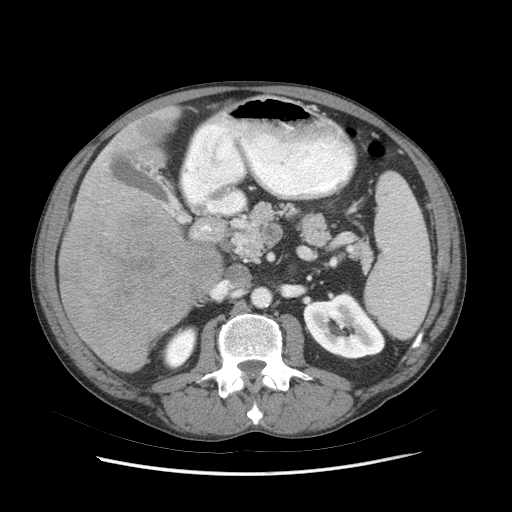
Contrast-enhanced abdominal CT (liver protocol), one axial slice; slice 31 of 89 in the series (ordered by position); reconstruction kernel STANDARD; 140 kVp; soft-tissue window (W 400 / L 40 HU); 2.5 mm slice thickness; 512 × 512 image matrix, field of view 380 × 380 mm. Case-level facts recorded for this patient, not image findings: diagnosis: hepatocellular carcinoma (patient treated with transarterial chemoembolisation; whether this scan precedes or follows treatment is not stated here); TNM stage (as recorded): Stage-IIIB; Child-Pugh class: A; tumour differentiation: moderately differentiated; tumour nodularity: multinodular.
Outlined on this slice (semi-automatic segmentation, software-assisted and operator-edited):
- liver parenchyma outside the tumour (the mass and vessels are separate outlines, so this box may not span the whole liver): box from (x=58, y=106) to (x=222, y=372) px
- mass: (x=60, y=207)–(x=223, y=370)
- liver vessels: (x=104, y=163)–(x=167, y=208)